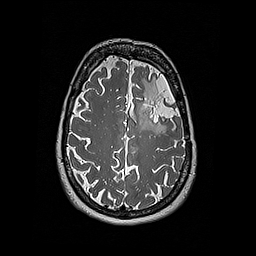
Brain MRI from a brain-tumour surgery series, one axial slice; slice 132 of 192 in the series (ordered by position); 256 × 256 image matrix, field of view 250 × 250 mm. From the clinical record (not read from this slice): histopathology: Oligodendroglioma; WHO grade: 2; IDH mutation: yes.
Annotated regions visible in this slice (expert manual segmentation):
- tumour: bounding box [x1, y1, x2, y2] px = [133, 79, 158, 131]